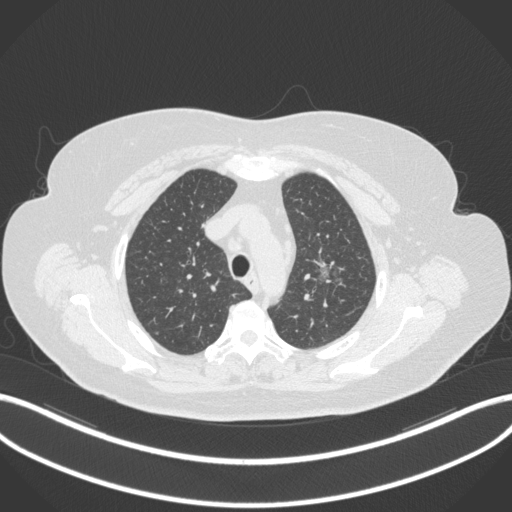
Chest CT, one axial slice. Position 260 of 310 along the scan axis. 120 kVp. Lung window (W 1500 / L -600 HU). 1 mm slice thickness. 512 × 512 image matrix. Female patient, age 70 years. Case-level facts recorded for this patient, not image findings: clinical TNM (as recorded): T1c N0 M0.
Outlined on this slice (bounding box drawn by a radiologist):
- lung tumour (recorded histology: adenocarcinoma): bounding box <311,251,340,289> (left, top, right, bottom; pixels)